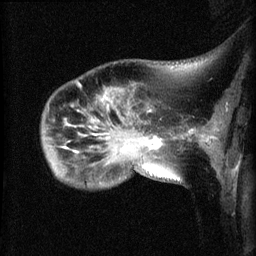
Breast MRI (dynamic contrast-enhanced), one sagittal slice. Slice 14 of 60 in the series (ordered by position). Dynamic contrast-enhanced series, image 2 of 3 at this slice position (ordered by acquisition). 1.5 T. TE 4.2 ms, TR 8.2 ms. 256 × 256 image matrix, field of view 180 × 180 mm. Female patient, age 50 years.
Outlined on this slice (semi-automatic segmentation, software-assisted and operator-edited):
- analysis volume of interest (the breast-tissue region the enhancement analysis was run in; not a lesion): bounding box (x1, y1, x2, y2) in pixels: (41, 85, 169, 187)
- tumour enhancement mask (voxels above the 70 % enhancement threshold inside the analysis volume of interest): (145, 136, 162, 150)